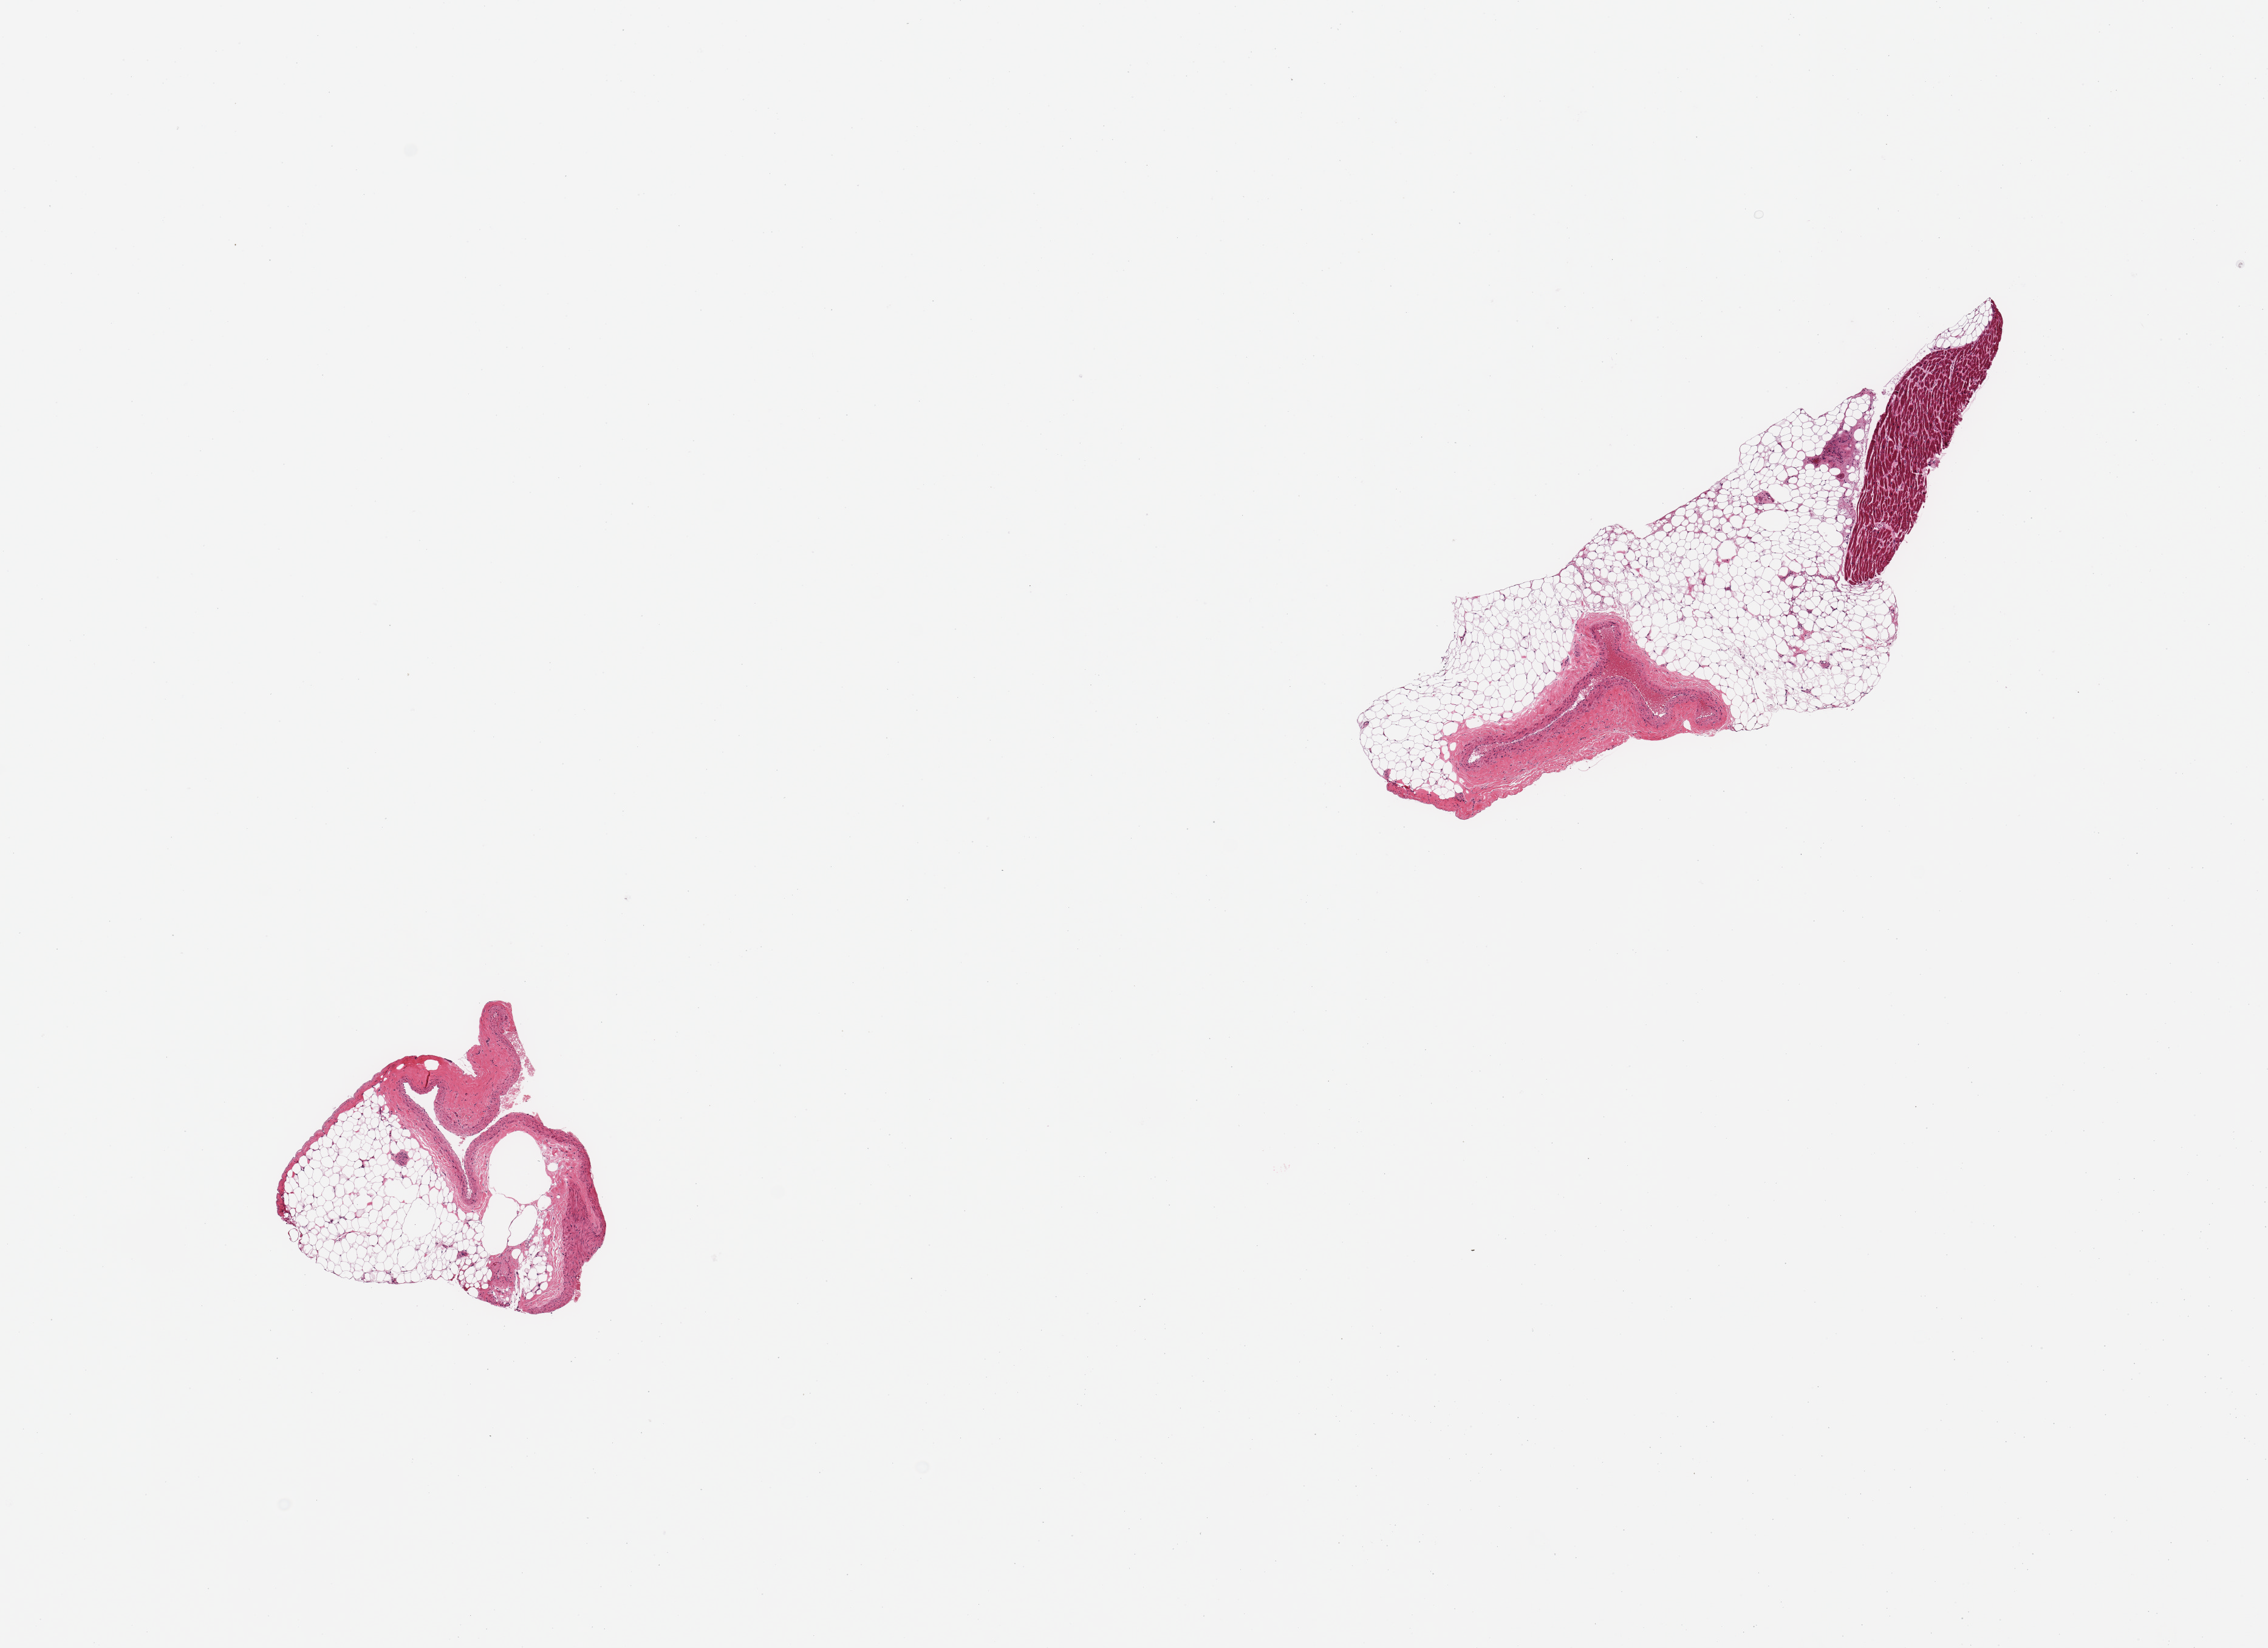
Whole-slide image, hematoxylin and eosin (H&E) stain — whole scanned area (about 14.8 x 10.7 mm) shown as a low-resolution overview. PAXgene-fixed paraffin-embedded (PFPE) section. Section of coronary artery (target tissue). Tissue donor sample. Donor: male.
Pathologist's review note for this sample: 2 pieces; patent vessels; attached ~1 mm fat and fat with myocardium.